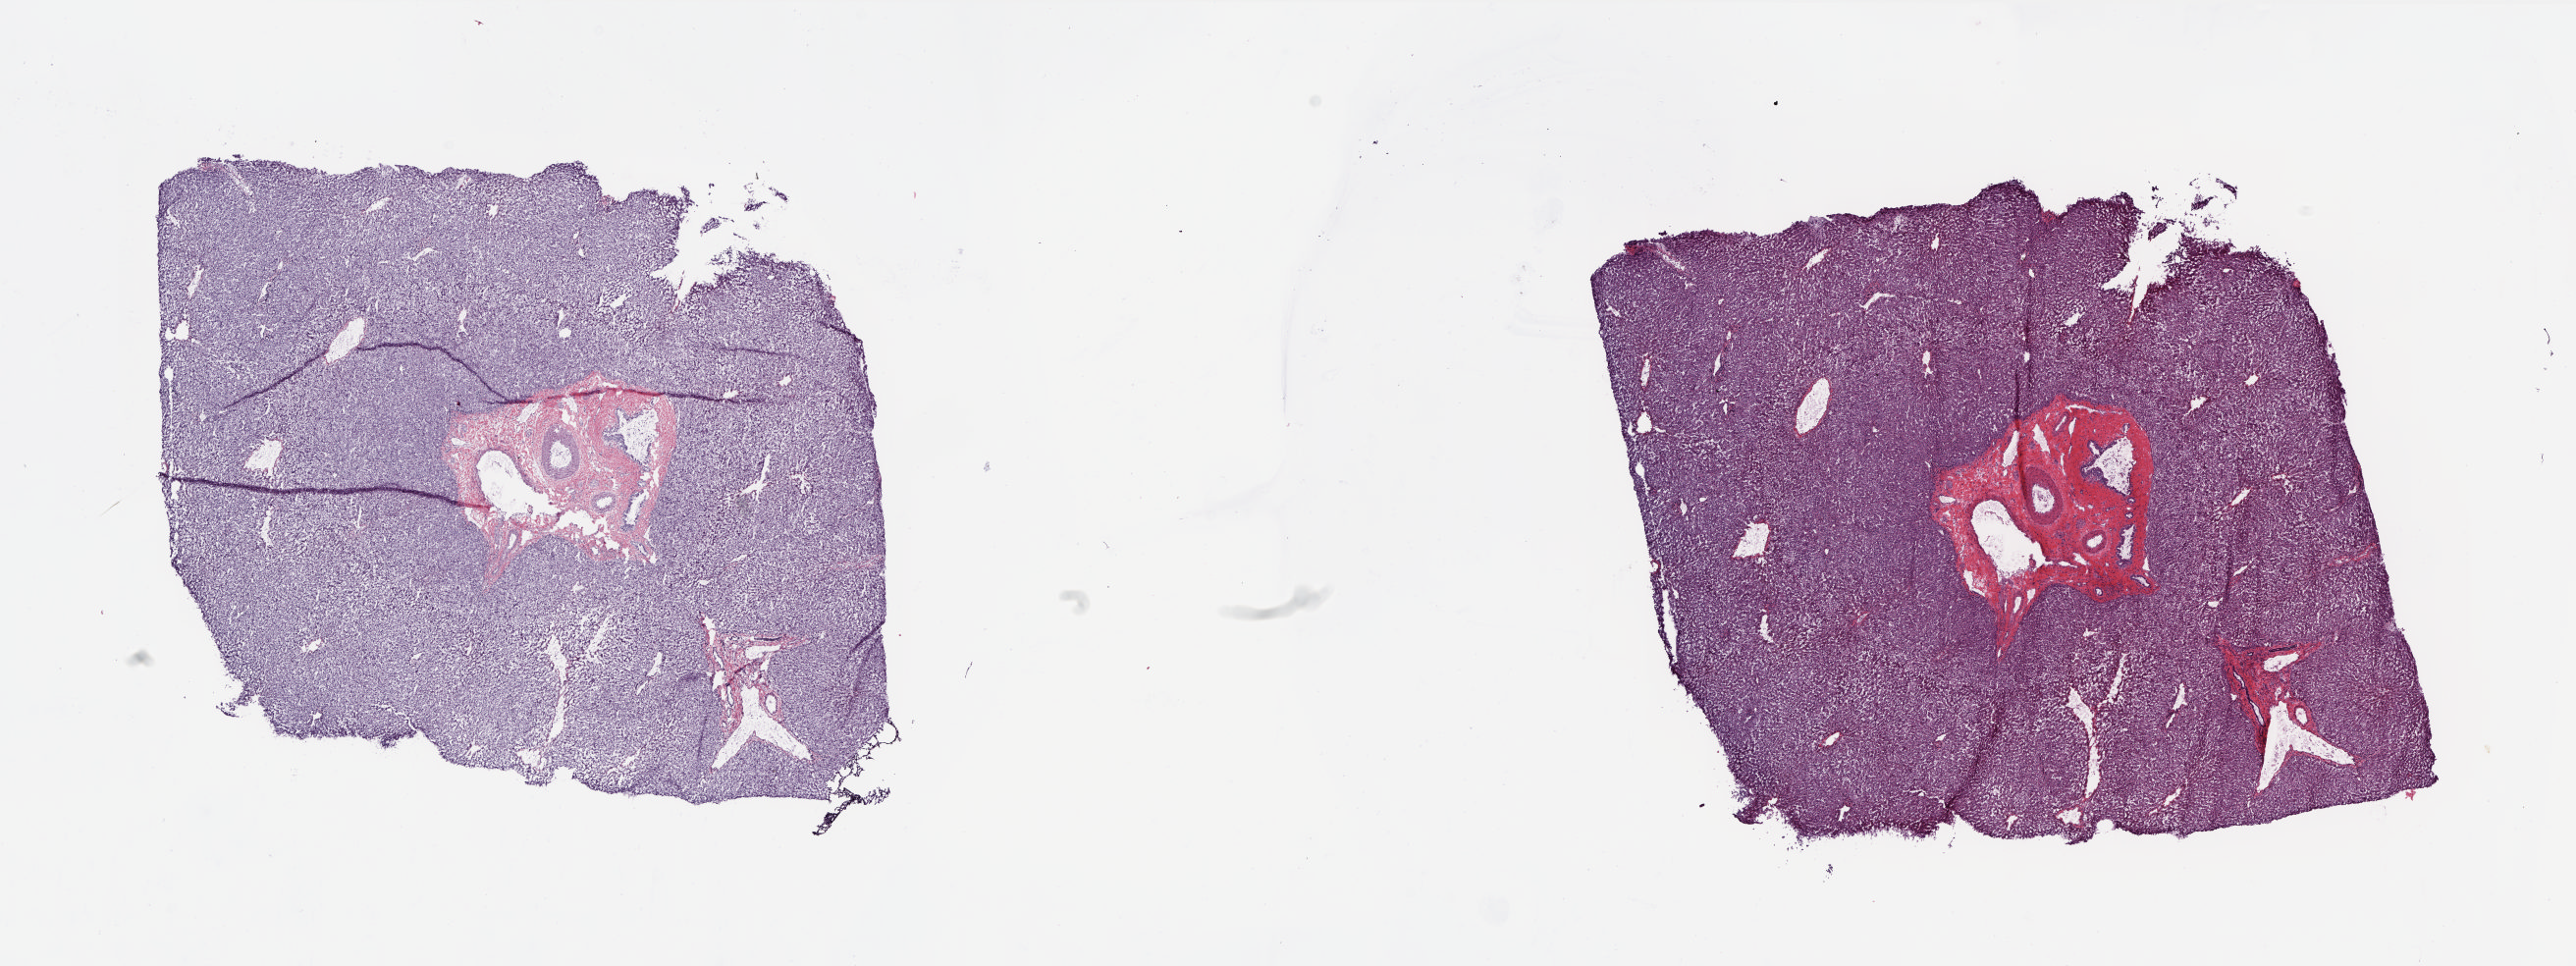
Whole-slide histology image, H&E, a low-resolution overview of the entire scanned area, about 21.2 x 7.9 mm (acquisition: 20x scan), frozen section, liver, solid tissue normal (non-tumour tissue) sample. Male, age 25 years at initial diagnosis. Slide review estimates, as recorded: tumour cells 0%, tumour nuclei 0%, normal cells 100%, stromal cells 0%, necrosis 0%. Infiltration values recorded for this section: lymphocyte infiltration 2%, monocyte infiltration 0%, neutrophil infiltration 0%.
This section: solid tissue normal (non-tumour) sample from the same patient. Patient diagnosis: Hepatocellular carcinoma, fibrolamellar.